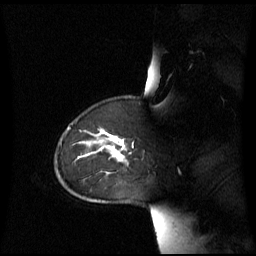
Breast MRI (dynamic contrast-enhanced), one sagittal slice; position 48 of 60 along the scan axis; dynamic contrast-enhanced series, image 2 of 3 at this slice position (ordered by acquisition); 1.5 T; TE 4.2 ms, TR 8.4 ms; 2.8 mm slice thickness; 256 × 256 image matrix, field of view 270 × 270 mm. Patient: female, 43 years. Case-level facts recorded for this patient, not image findings: setting: breast cancer imaged before/during neoadjuvant chemotherapy; receptor status: triple-negative.
Annotated regions visible in this slice (semi-automatic segmentation, software-assisted and operator-edited):
- analysis volume of interest (the breast-tissue region the enhancement analysis was run in; not a lesion): box from (x=55, y=124) to (x=129, y=173) px
- tumour enhancement mask (voxels above the 70 % enhancement threshold inside the analysis volume of interest): (x=108, y=136)–(x=124, y=149)